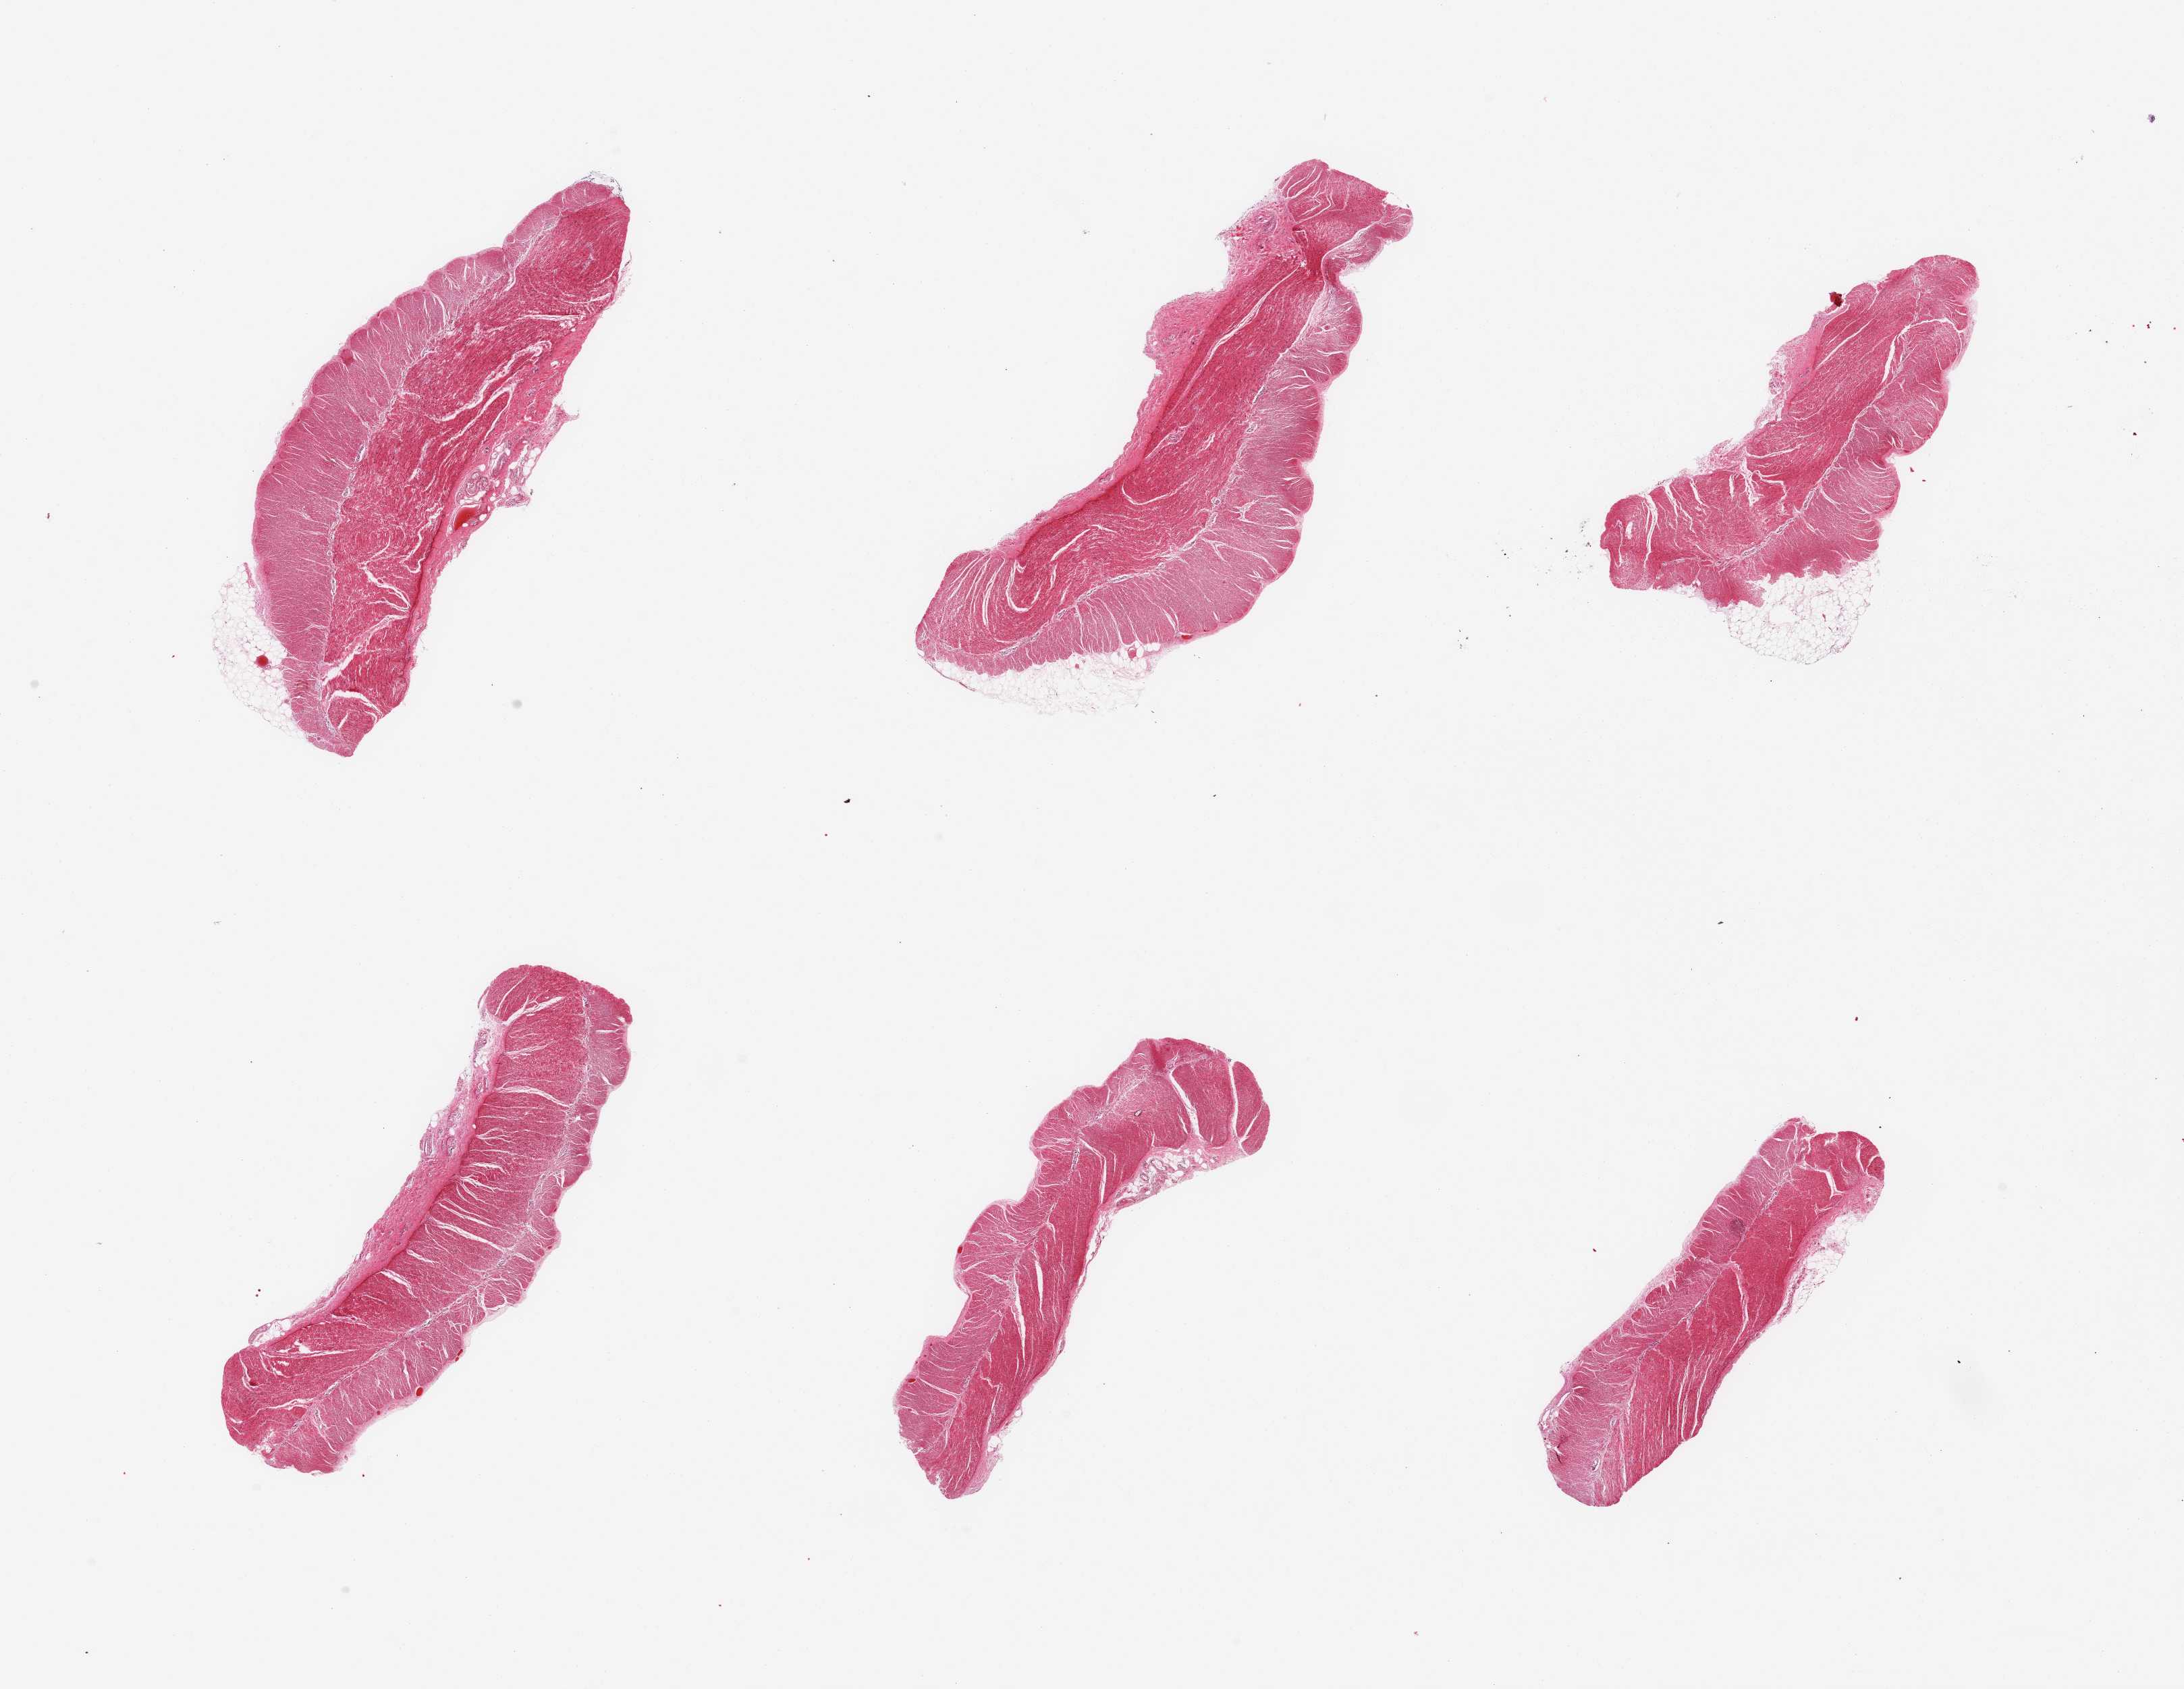
Haematoxylin and eosin whole-slide image, shown as a low-resolution overview of the whole scanned area (about 25.6 x 19.8 mm, from a 20x scan), PAXgene-fixed paraffin-embedded (PFPE) section, sampled site (target tissue): sigmoid colon, donor tissue sample. Donor: female.
Reviewer comment on this tissue sample: 6 pieces, confirmed target muscularis.